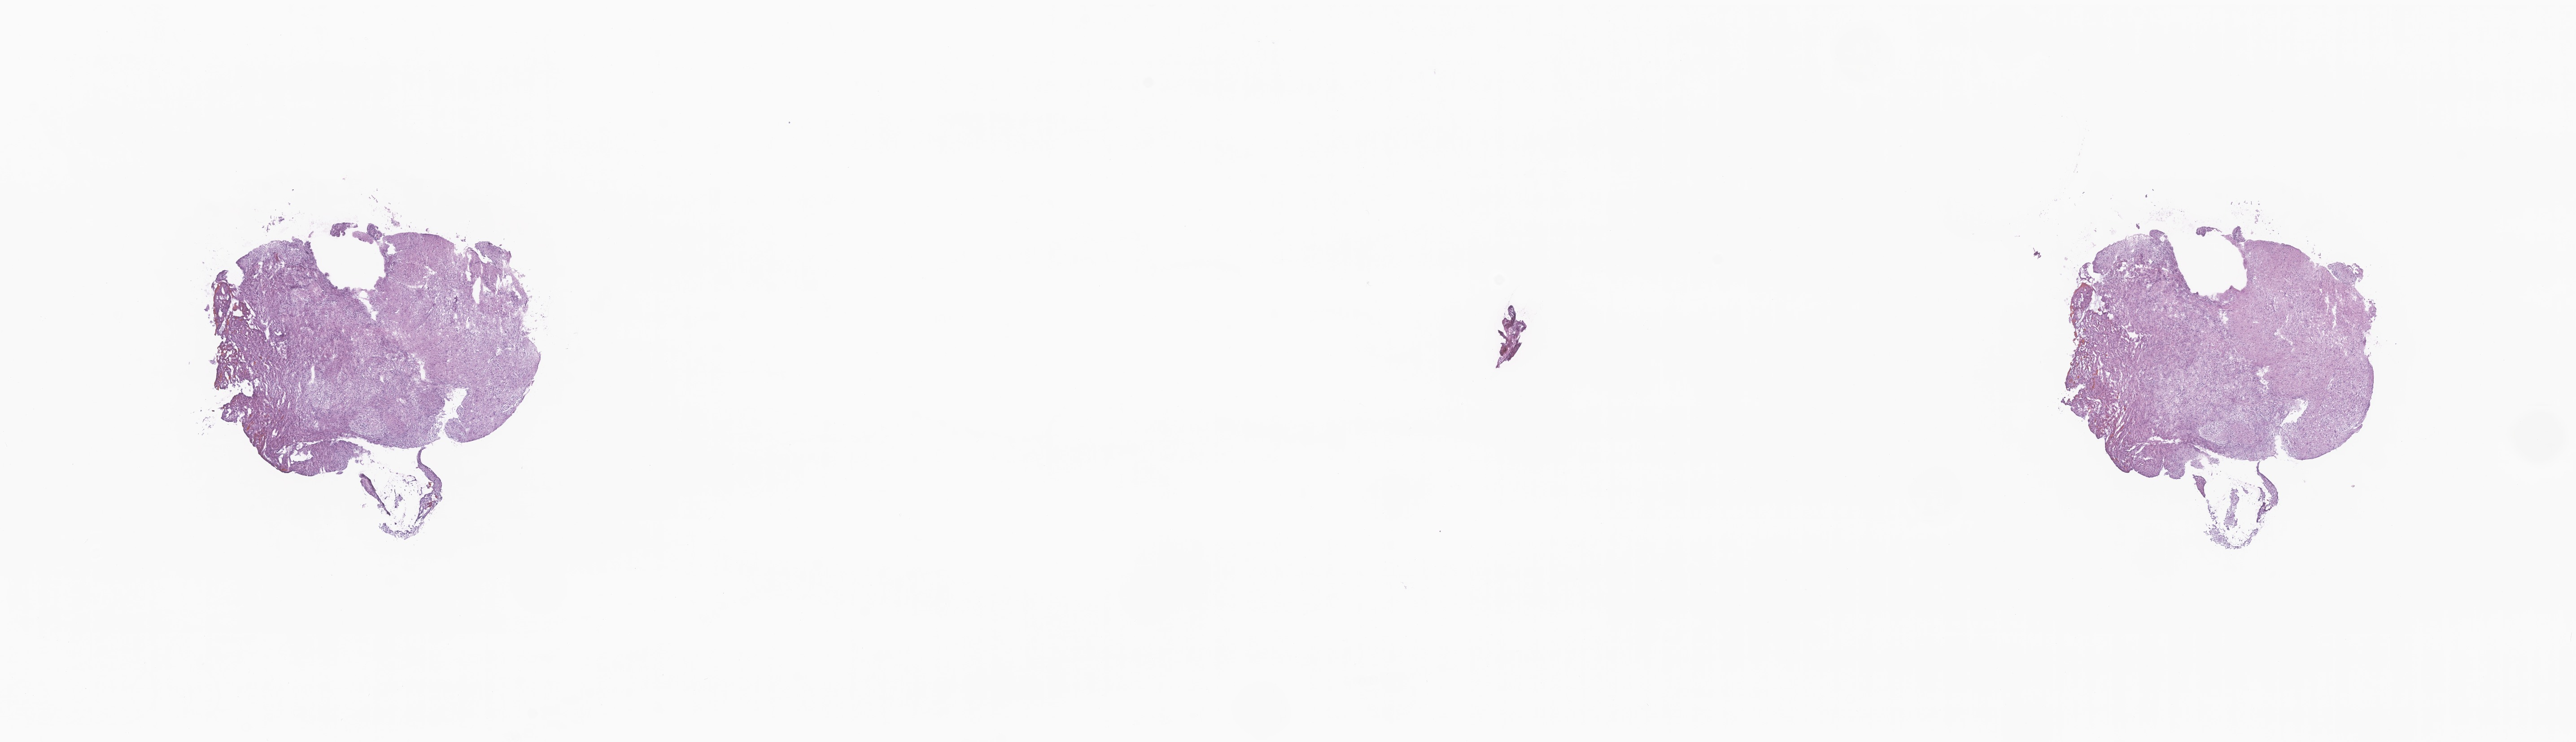
Haematoxylin and eosin whole-slide image of tumor tissue from the cerebrum — shown as a low-resolution overview of the whole scanned area (about 24.2 x 7.0 mm); frozen section. Patient female; age 202 days.
Recorded diagnosis: Astrocytoma, NOS.